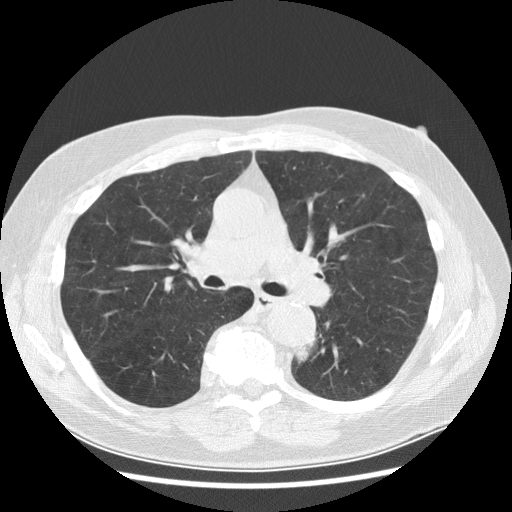
Low-dose screening chest CT, one axial slice; slice 172 of 282 in the series (ordered by position); 120 kVp; lung window (W 1500 / L -600 HU); 2.5 mm slice thickness; 512 × 512 image matrix.
Structures marked on this image (manually delineated by an expert):
- lesion 1 (tumor, lower lobe of left lung): bounding box (x1, y1, x2, y2) in pixels: (295, 346, 311, 363)